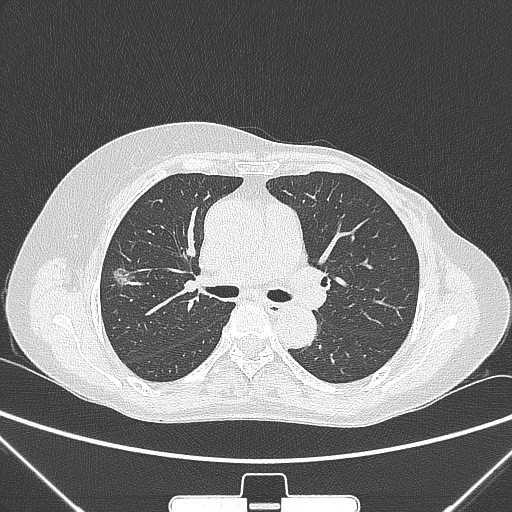
Chest CT, one axial slice; slice 156 of 265 in the series (ordered by position); 120 kVp; lung window (W 1500 / L -600 HU); 1 mm slice thickness; 512 × 512 image matrix, field of view 350 × 350 mm. Female patient, age 64 years. From the clinical record (not read from this slice): clinical TNM (as recorded): T1c N0 M0; histopathological grade: G1-2.
Annotated regions visible in this slice (bounding box drawn by a radiologist):
- lung tumour (recorded histology: adenocarcinoma): bounding box <110,262,137,290> (left, top, right, bottom; pixels)